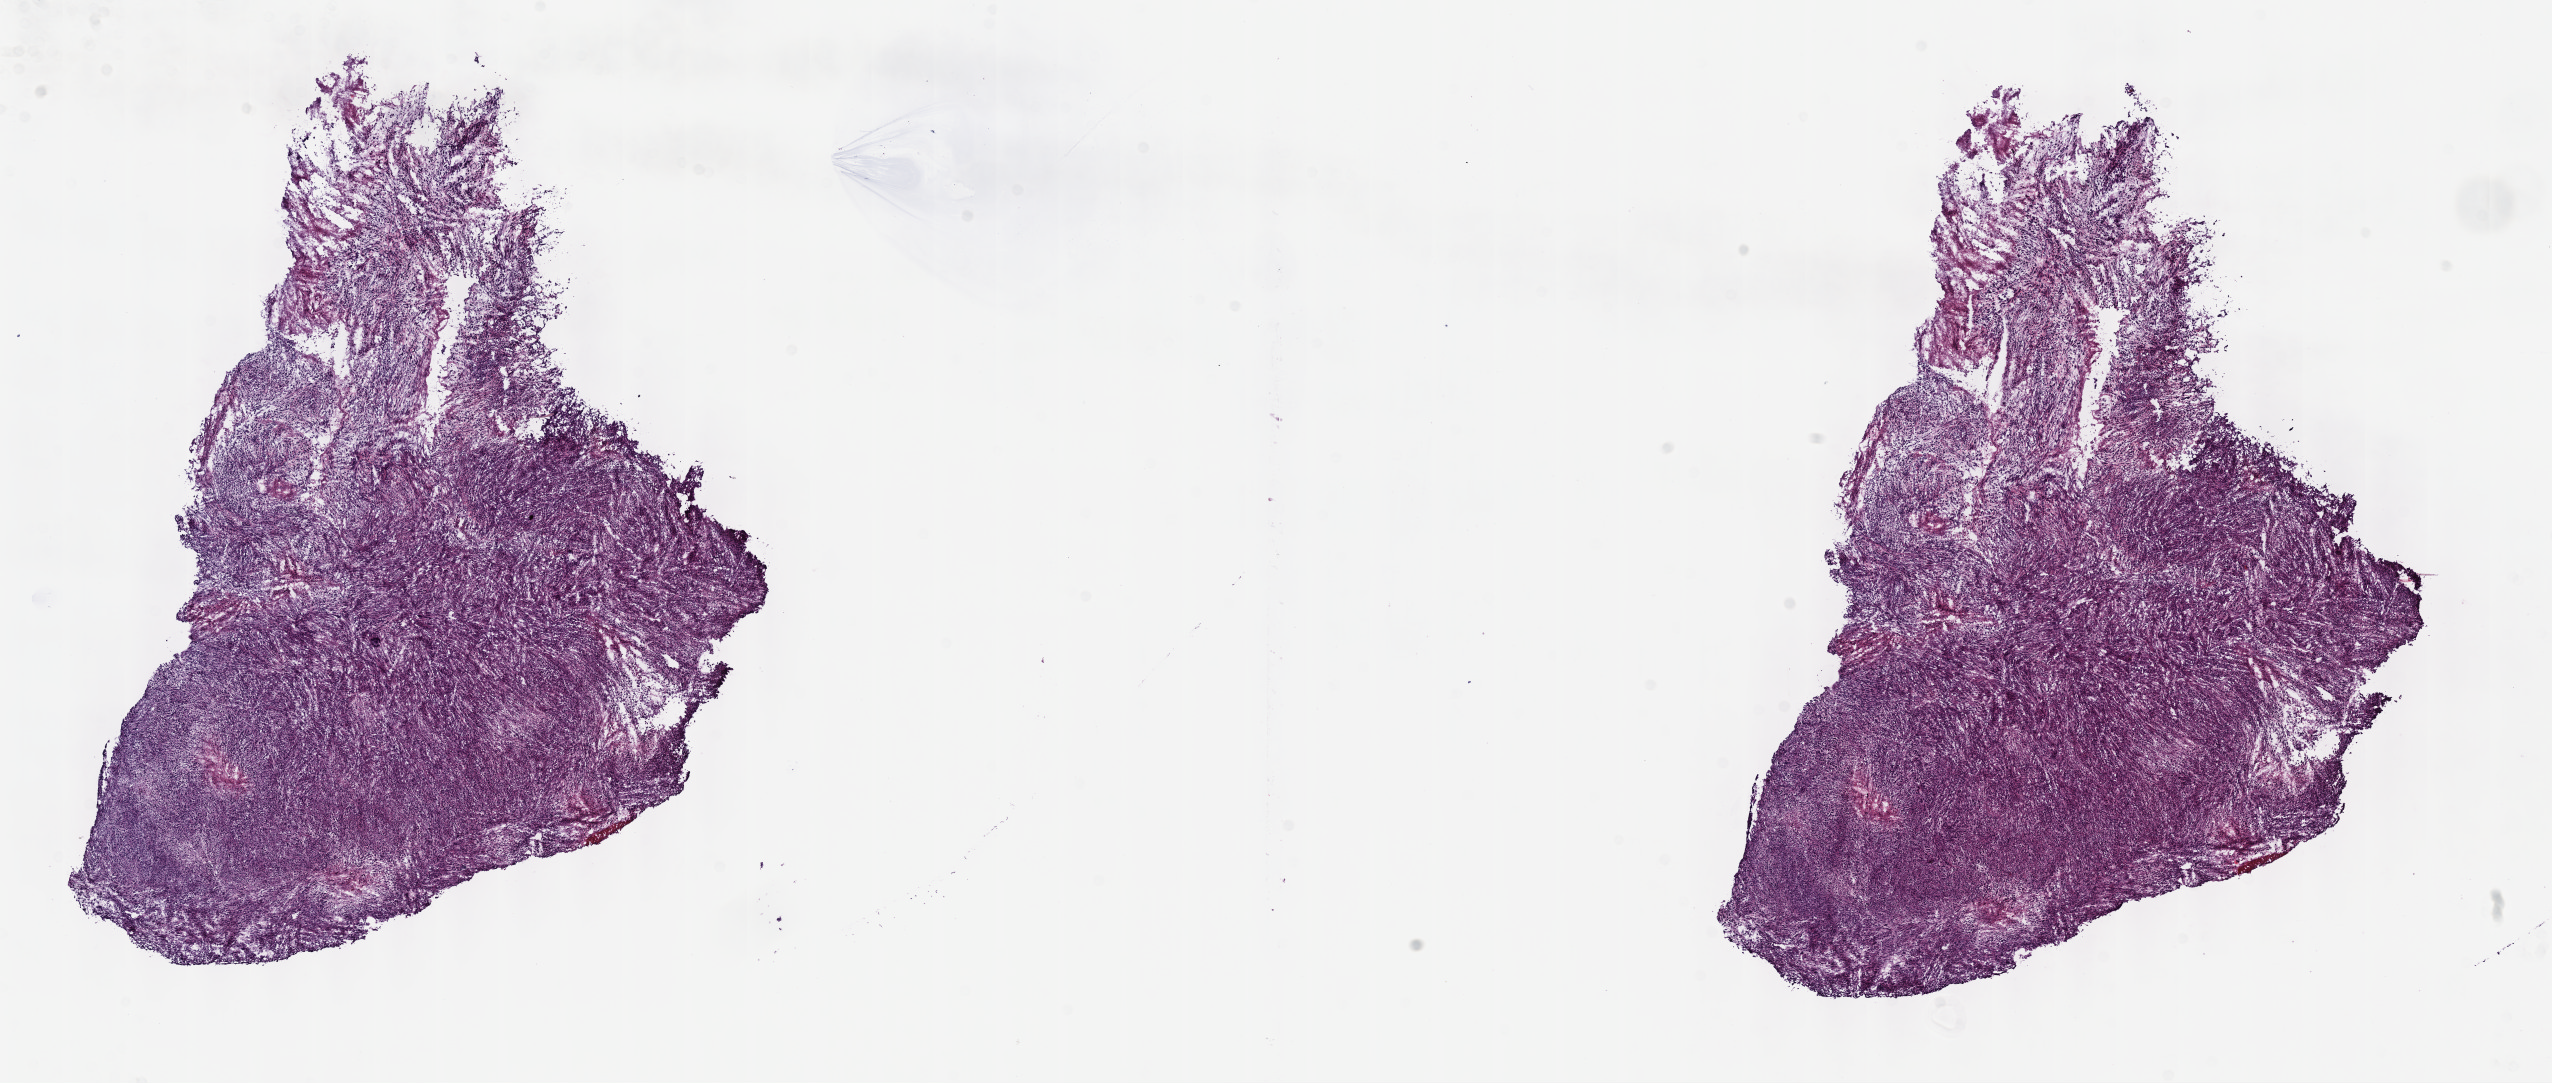
Whole-slide histology image, Hematoxylin and eosin (H&E) stained, a low-resolution overview of the entire scanned area, about 20.6 x 8.8 mm (from a 40x scan), frozen section, primary tumour sample from the connective, subcutaneous and other soft tissues. Female patient; age at initial diagnosis 70 years. Pathologist review of this section (percent, as recorded): tumour cells 100%, tumour nuclei 80%, normal cells 0%, stromal cells 0%, necrosis 0%. Infiltration values recorded for this section: lymphocyte infiltration 2%, monocyte infiltration 0%, neutrophil infiltration 0%.
Pathologic diagnosis: Undifferentiated sarcoma.